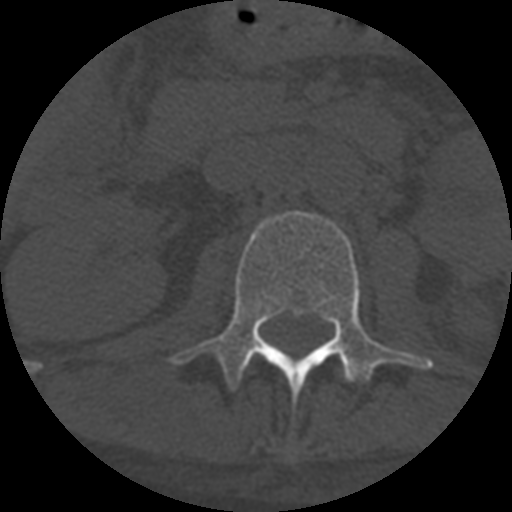
CT including the spine, one axial slice. Reconstruction kernel STANDARD. 120 kVp. One of 3 acquisitions stored at this slice position. Bone window (W 1800 / L 400 HU). 1.25 mm slice thickness. 512 × 512 image matrix, field of view 160 × 160 mm. Patient age 55 years. From the clinical record (not read from this slice): primary cancer: colon; vertebrae with lytic lesions (as recorded): T12, L1, L5.
Outlined on this slice (semi-automatically segmented with operator editing):
- L1 vertebra: bounding box <341,371,345,375> (left, top, right, bottom; pixels)
- L2 vertebra: <171,211,433,396>